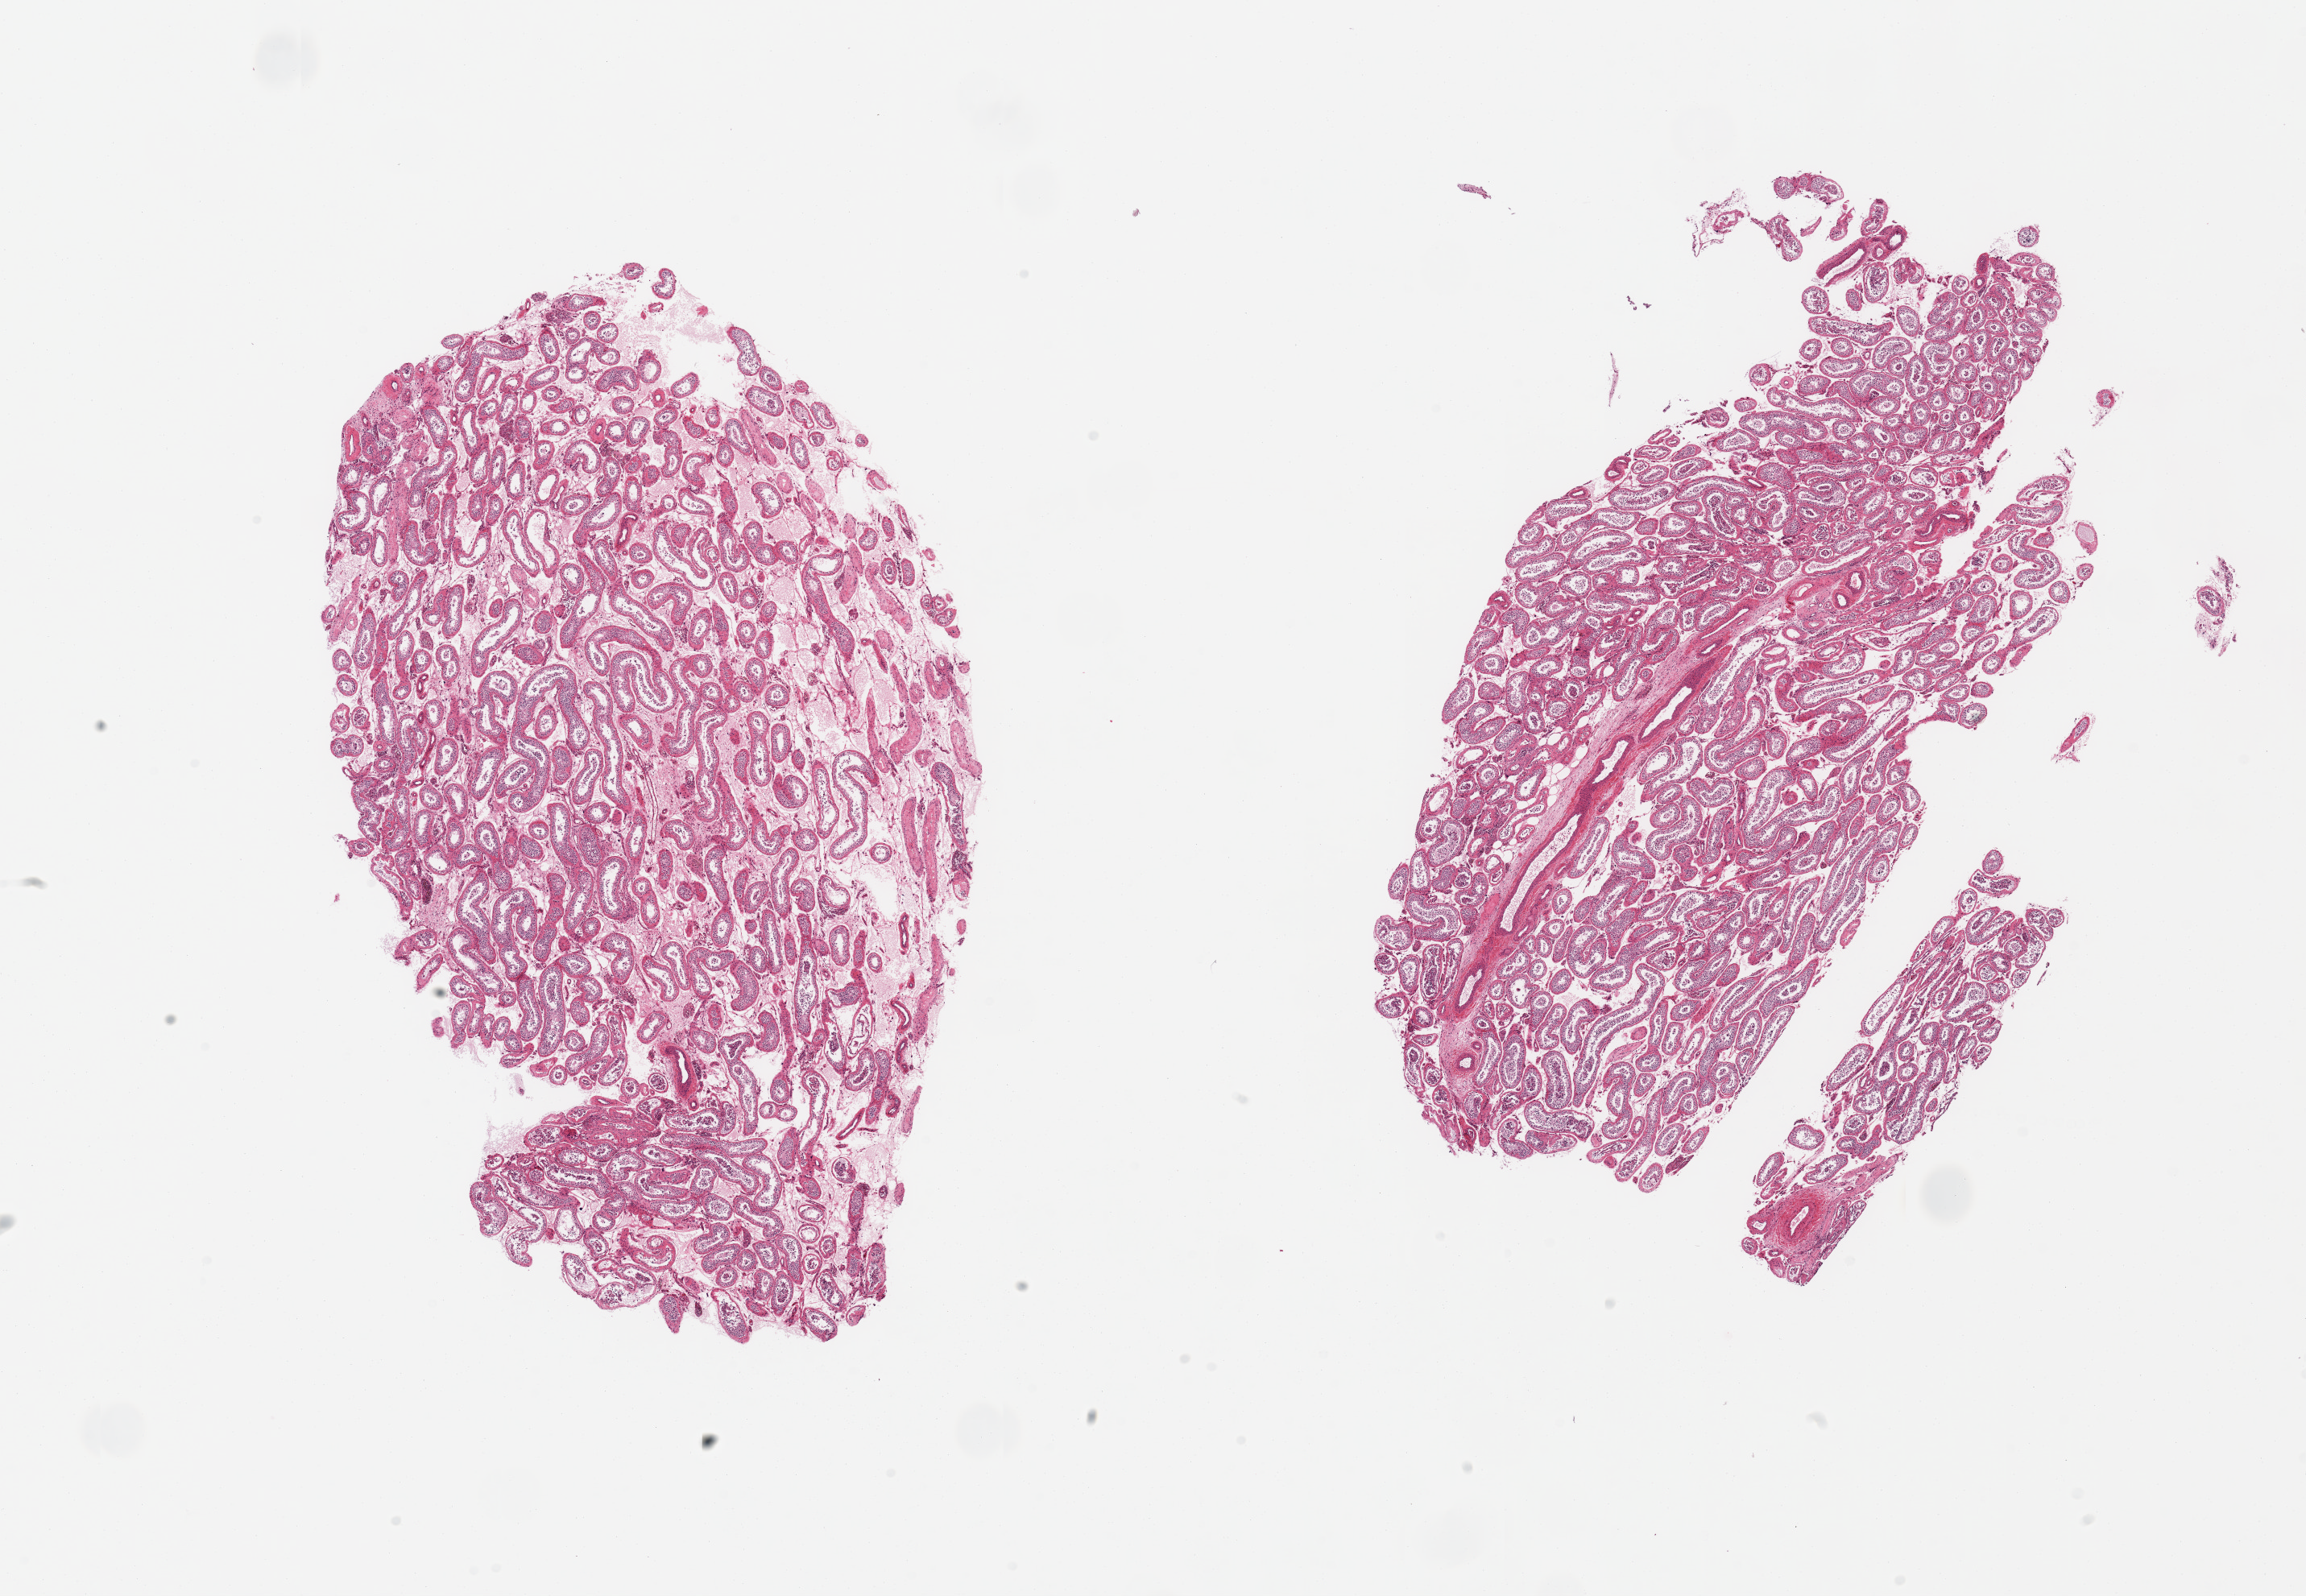
Digitized hematoxylin and eosin (H&E)-stained section, a low-resolution overview of the entire scanned area, about 22.6 x 15.7 mm. PAXgene-fixed paraffin-embedded (PFPE) section. Target tissue: testis. Donor tissue sample.
- reviewer comment on this tissue sample: 2 pieces, spermatogenesis appears markedly reduced